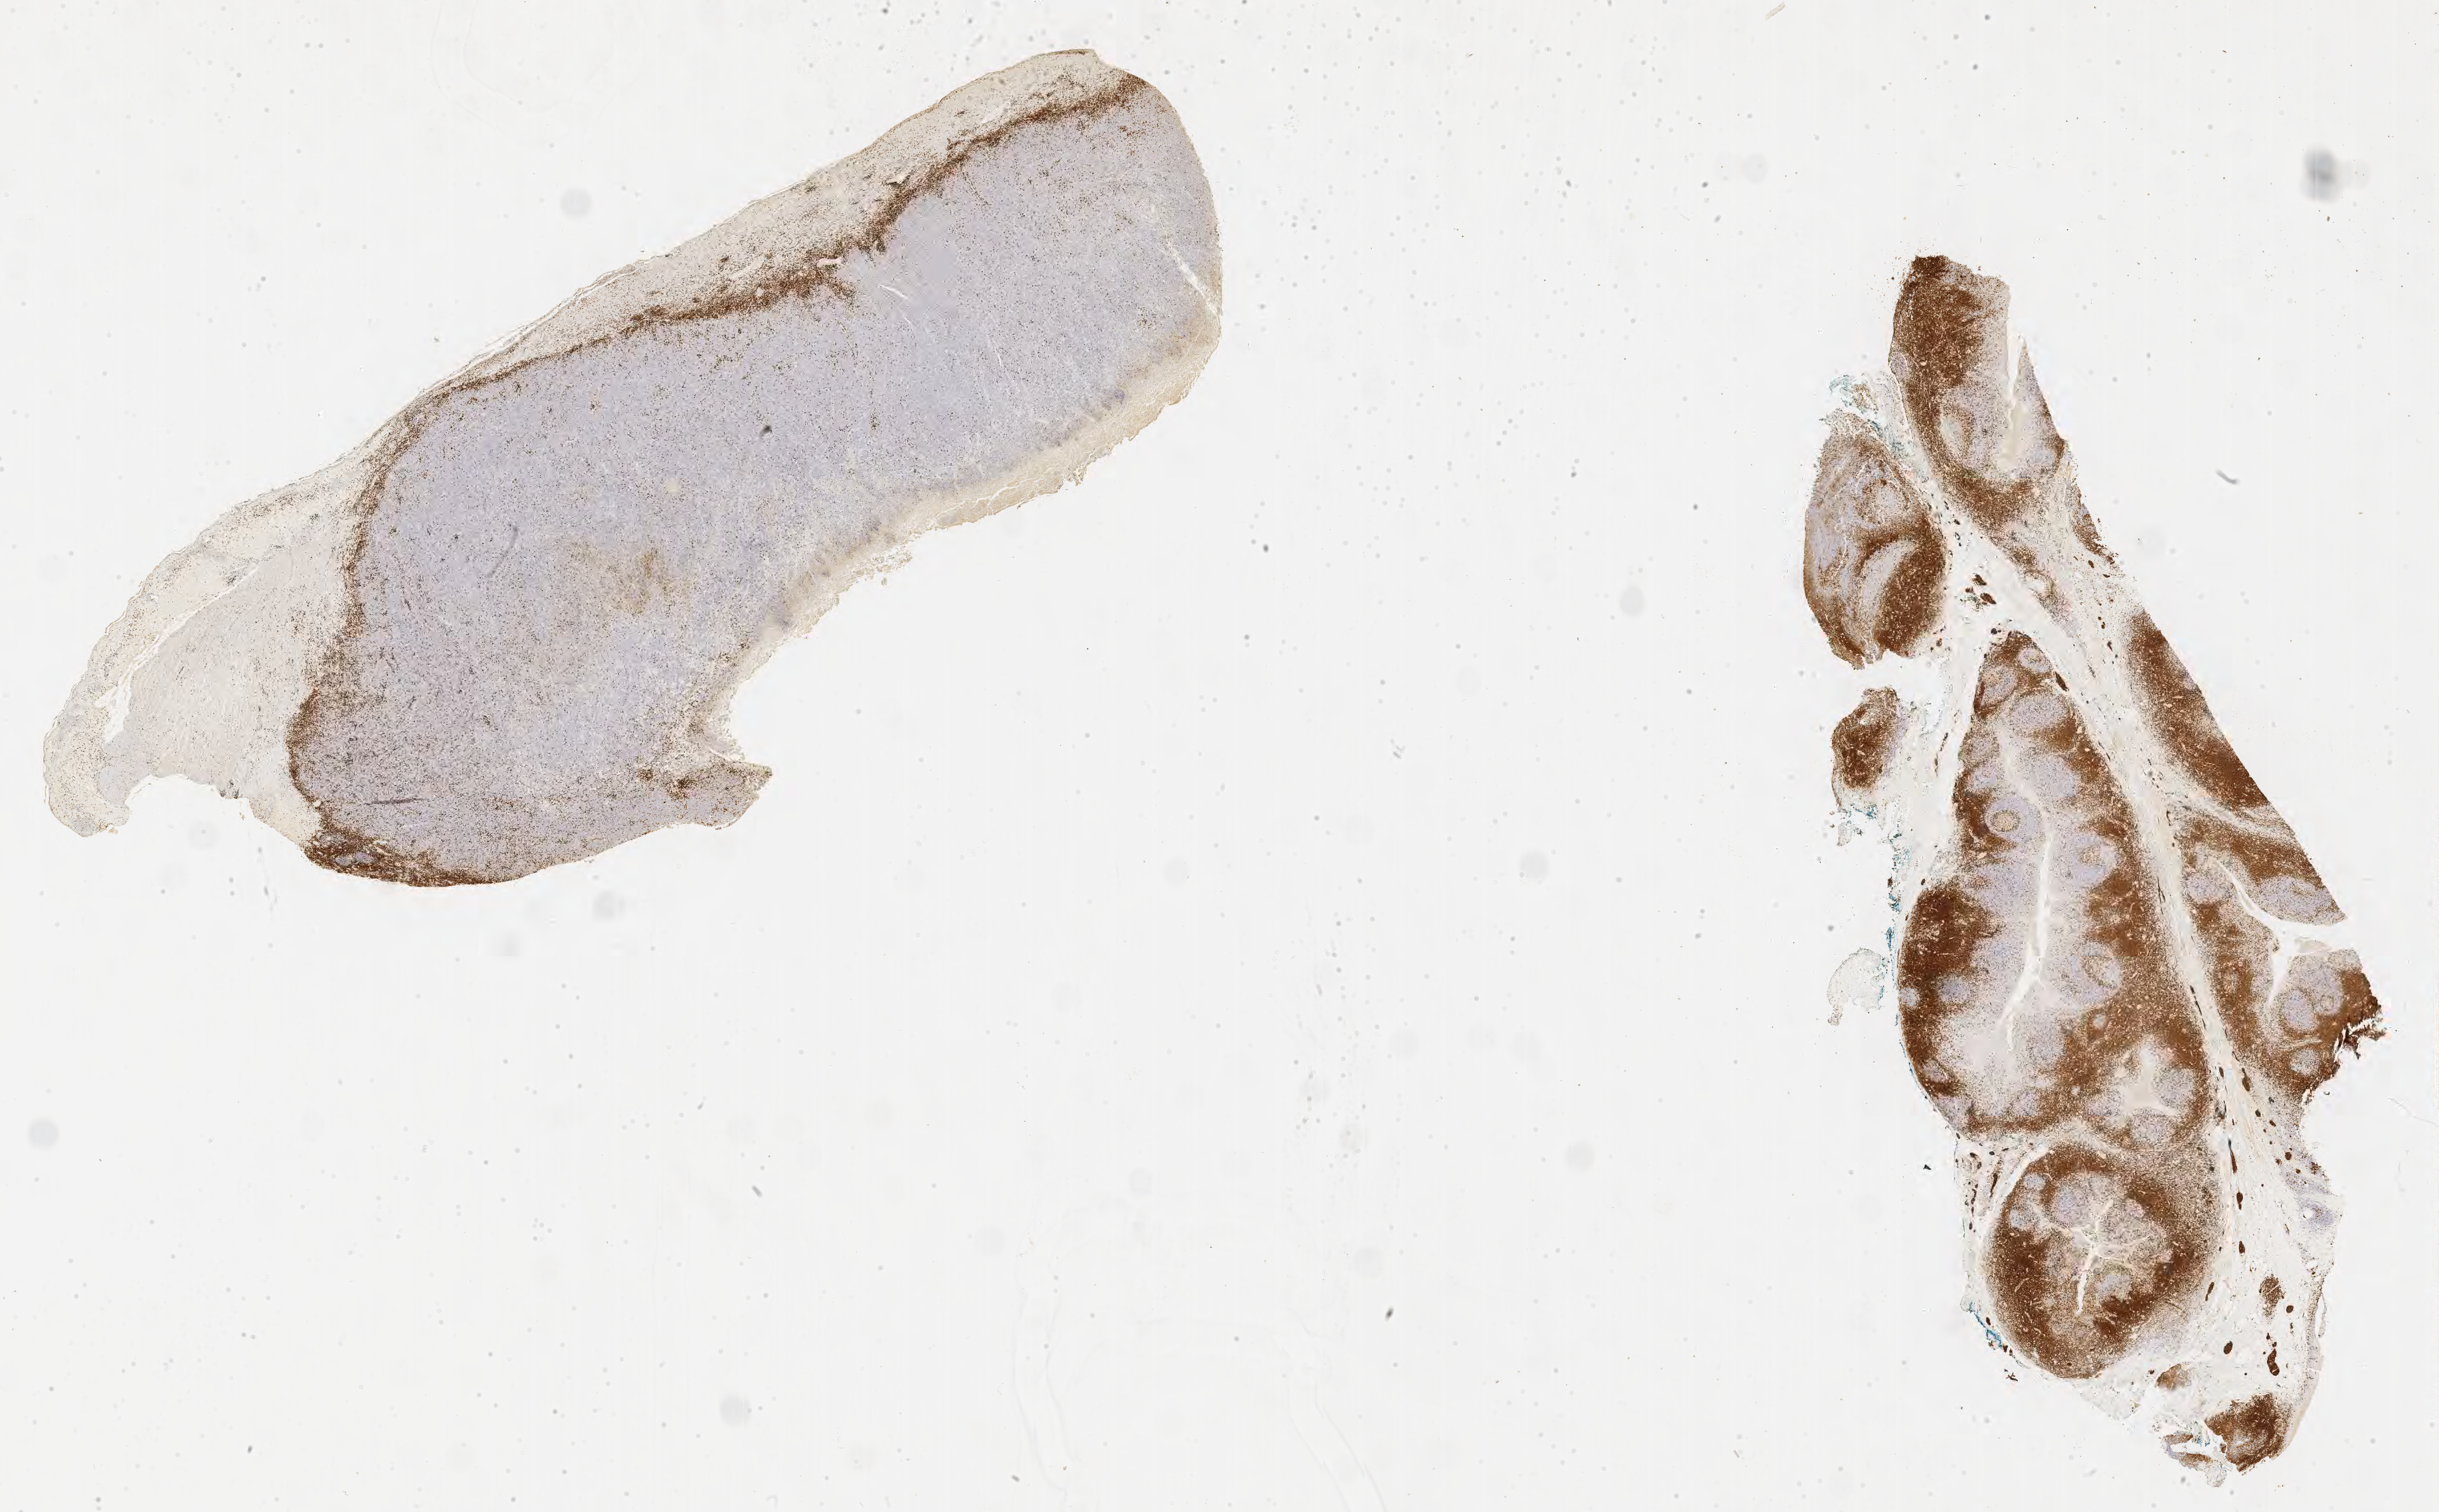
Immunohistochemistry (IHC) whole-slide image stained for CD3, whole scanned area (about 29.7 x 18.4 mm) shown as a low-resolution overview. Specimen: tumor tissue. Site: small intestine. Patient: male, age at initial diagnosis 3 years.
Histologic diagnosis: Burkitt lymphoma, NOS.